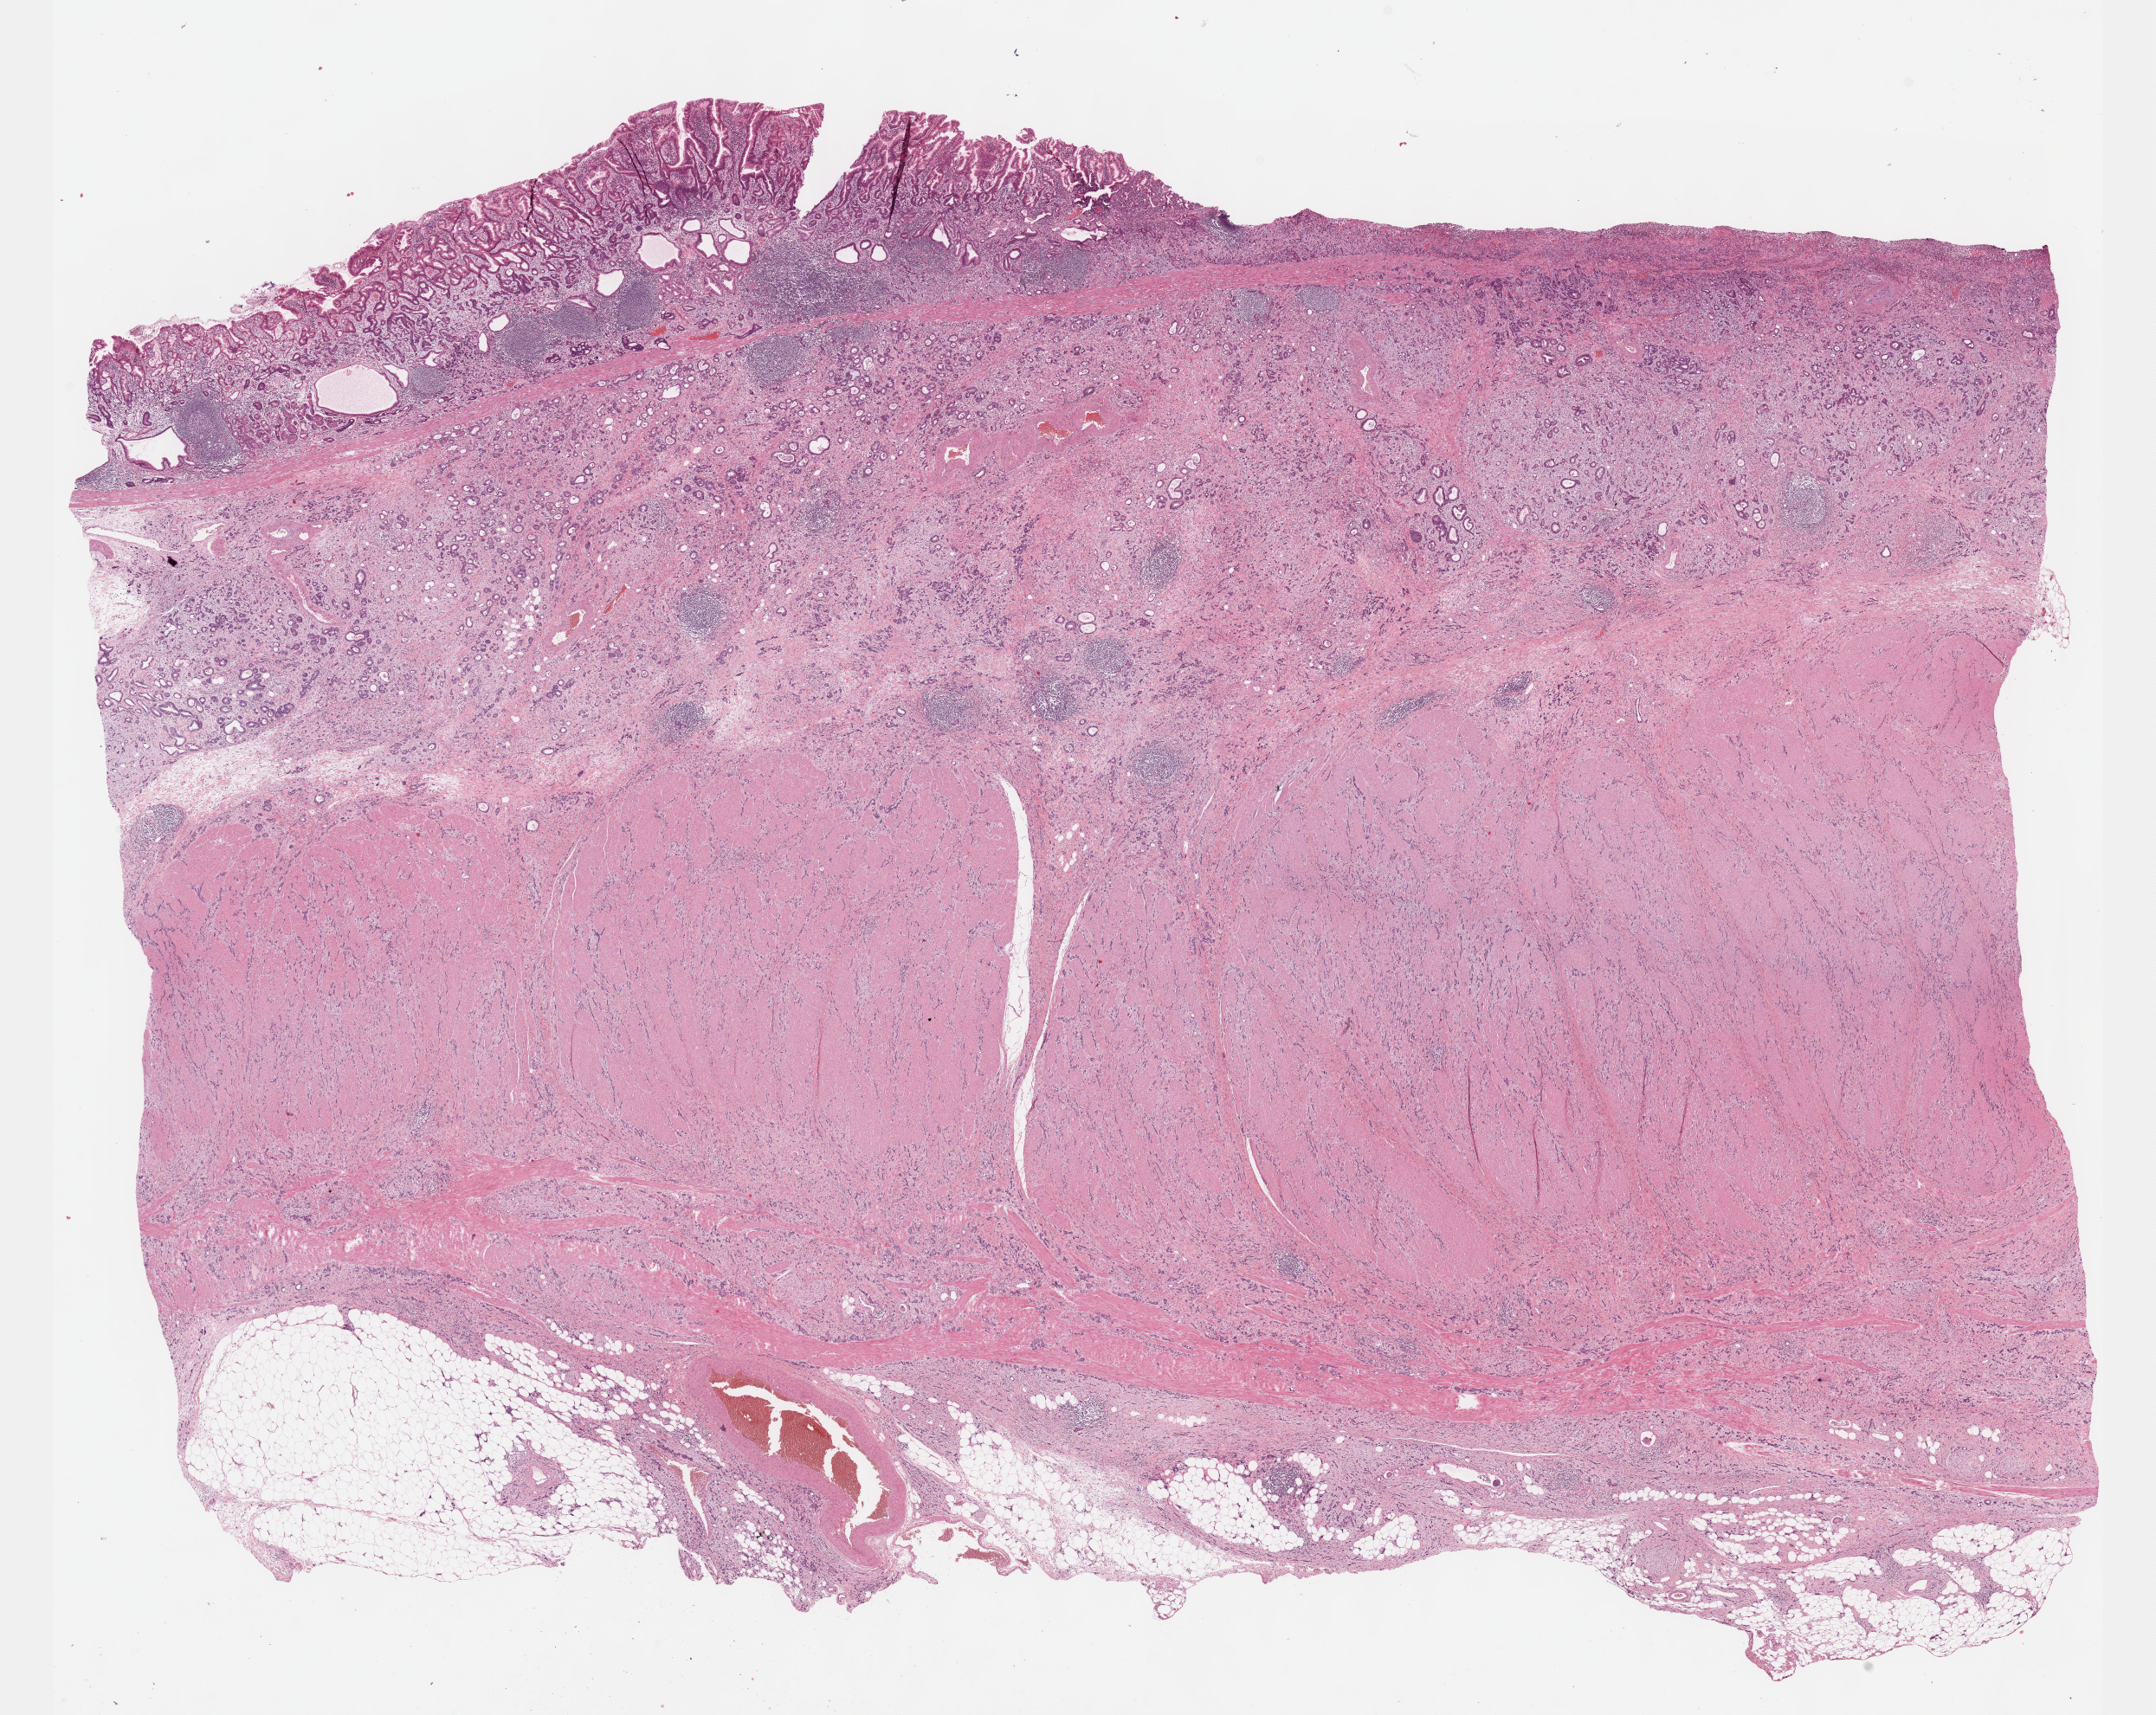
Whole-slide histology image, Hematoxylin and eosin (H&E) stained — a low-resolution overview of the entire scanned area, about 20.1 x 16.0 mm (slide scanned at 40x); FFPE section; stomach, primary tumour sample. Male, age 69 years at initial diagnosis.
Histologic diagnosis: Adenocarcinoma, NOS (body of stomach).